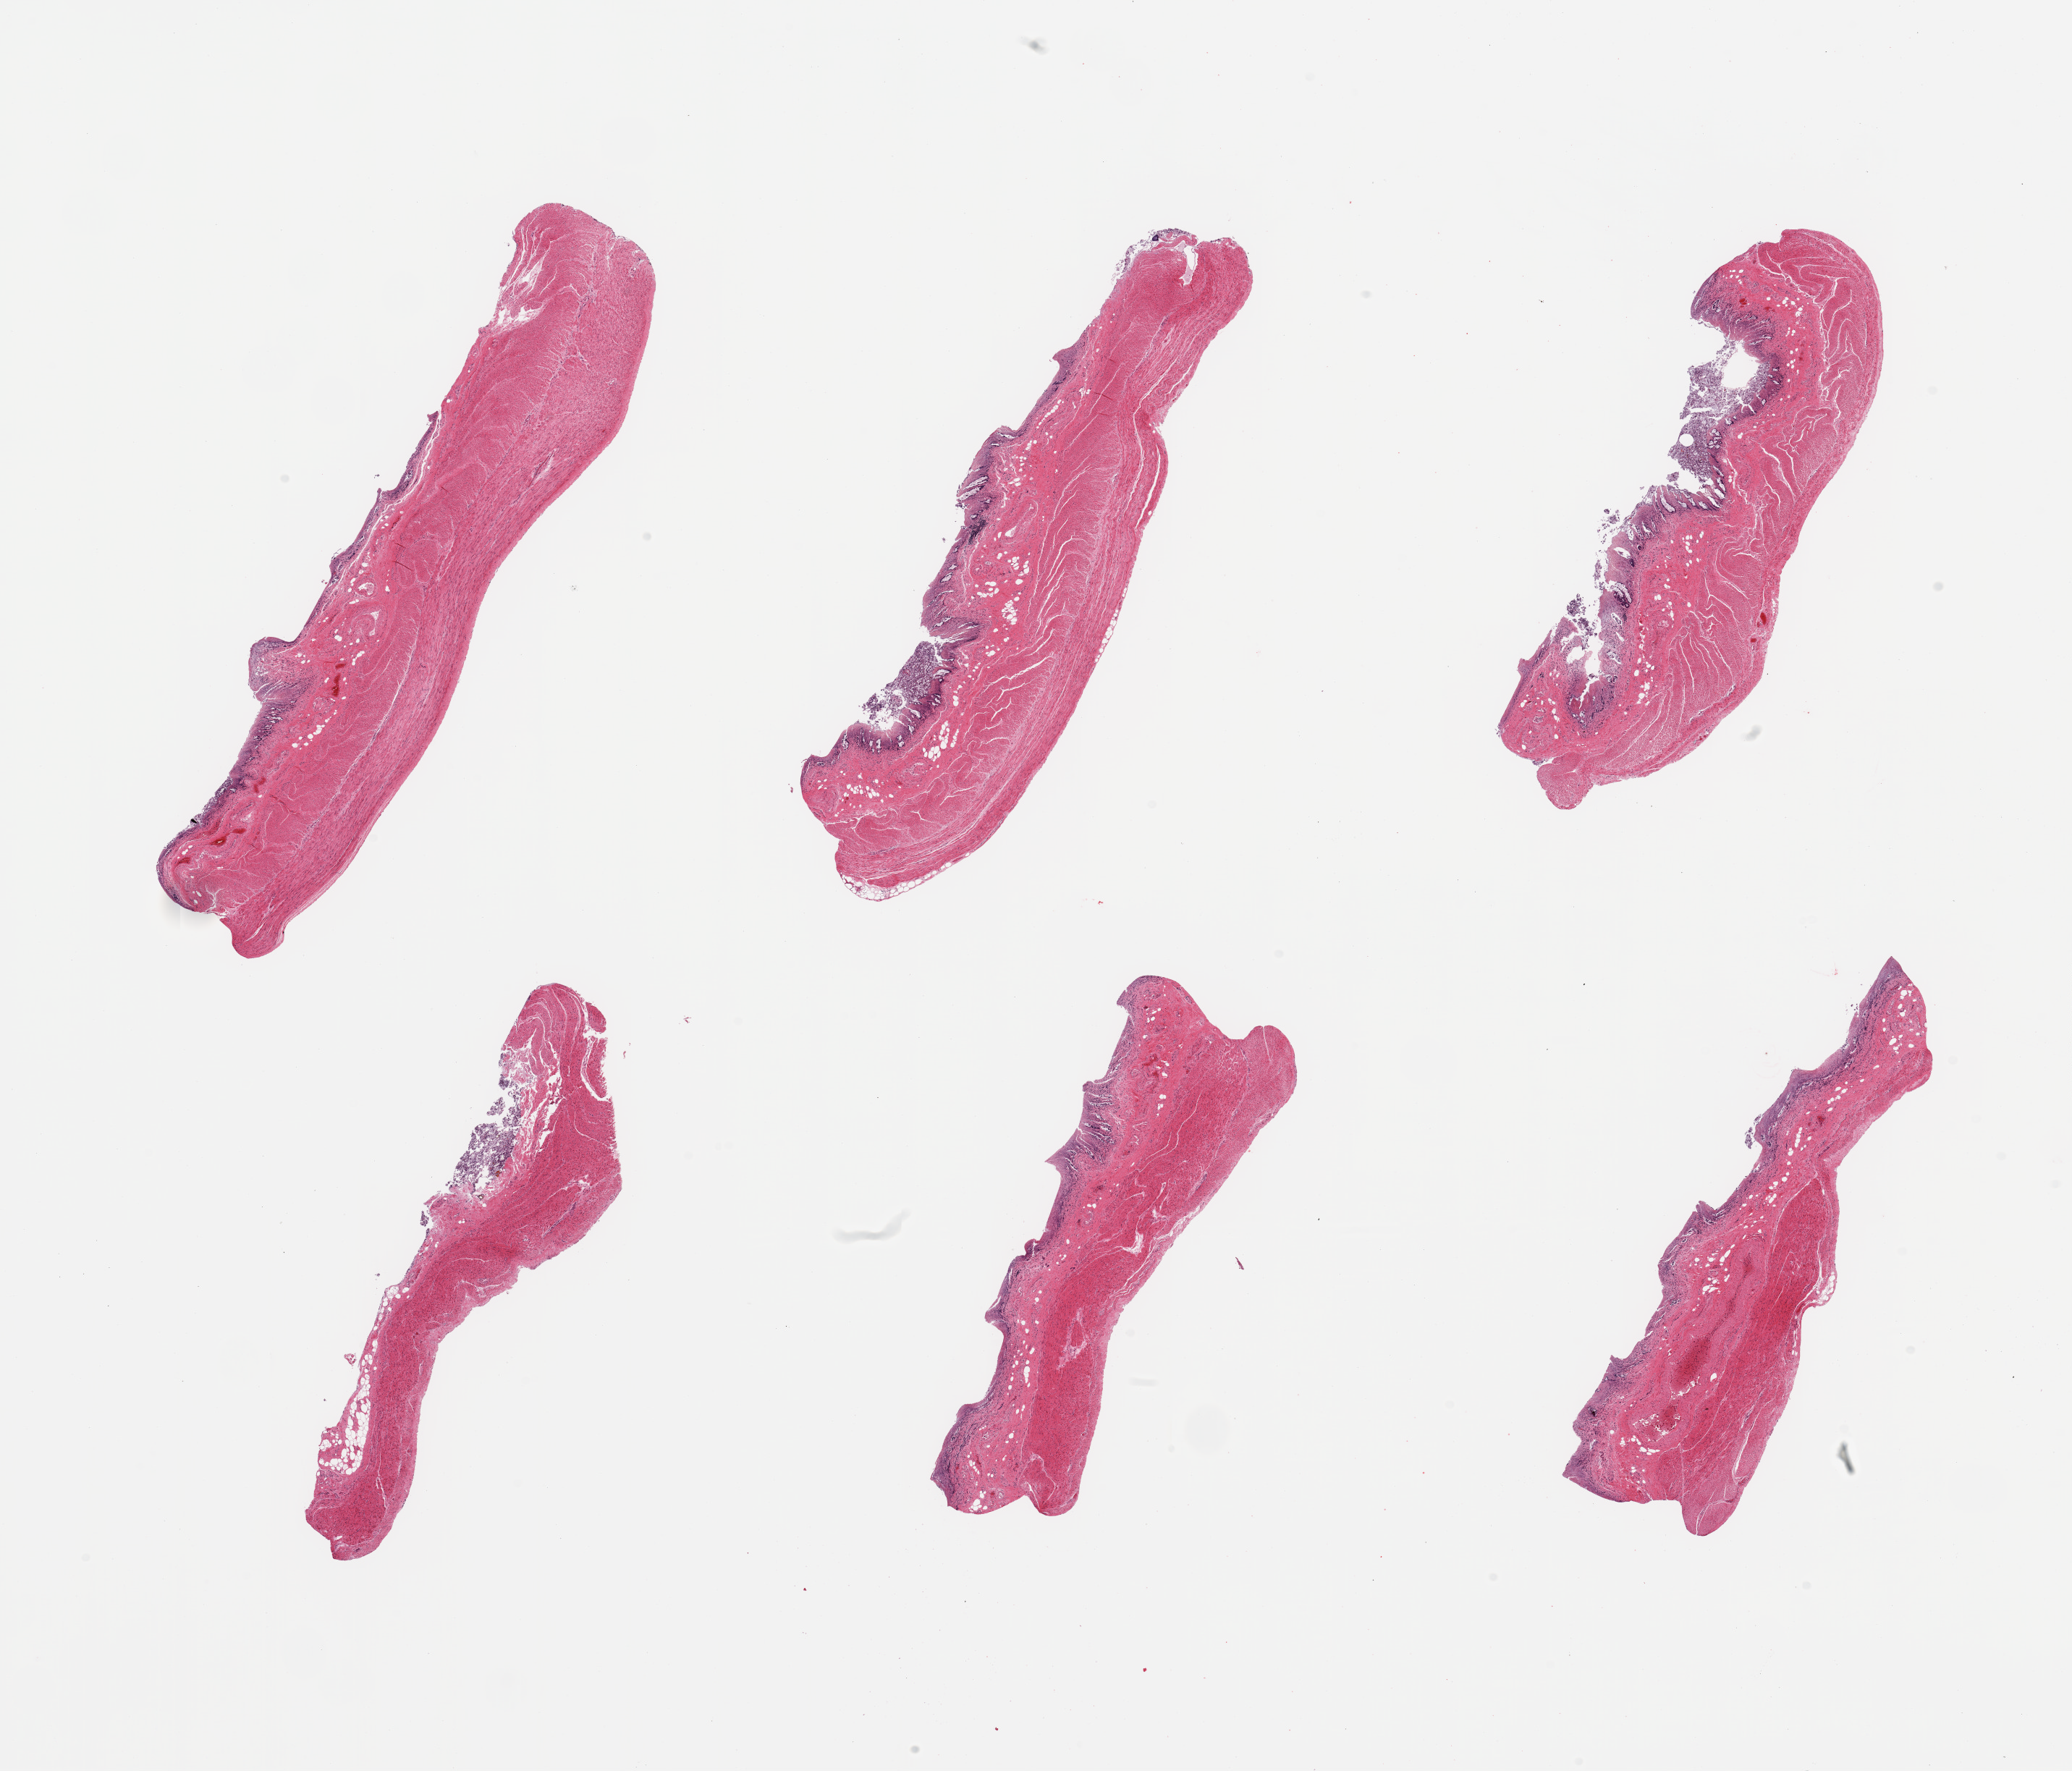
Digitized H&E-stained section, brightfield, whole scanned area (about 22.6 x 19.4 mm) shown as a low-resolution overview; PAXgene-fixed, paraffin-embedded tissue; section of transverse colon (target tissue); donor tissue sample.
• pathologist's review note for this sample: 6 pieces, mucosa largely slouhged/advanced autolysis